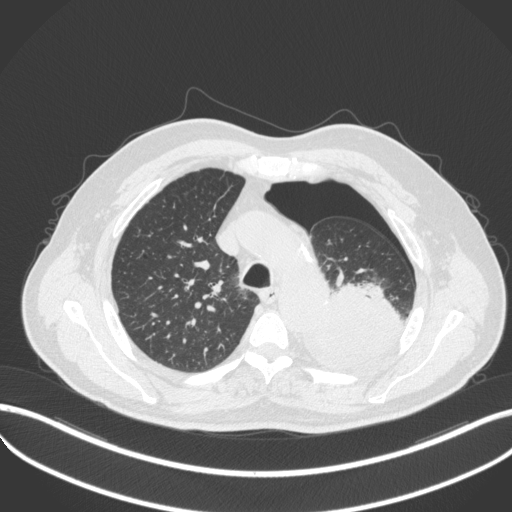
Chest CT, one axial slice. Slice 378 of 466 in the series (ordered by position). Reconstruction kernel B31f. 120 kVp. Lung window (W 1500 / L -600 HU). 1 mm slice thickness. 512 × 512 image matrix, field of view 400 × 400 mm. Patient: male, 76 years. From the clinical record (not read from this slice): clinical TNM (as recorded): T3 N0 M1b.
Structures marked on this image (bounding box drawn by a radiologist):
- lung tumour (recorded histology: adenocarcinoma): bounding box [x1, y1, x2, y2] px = [297, 278, 408, 371]